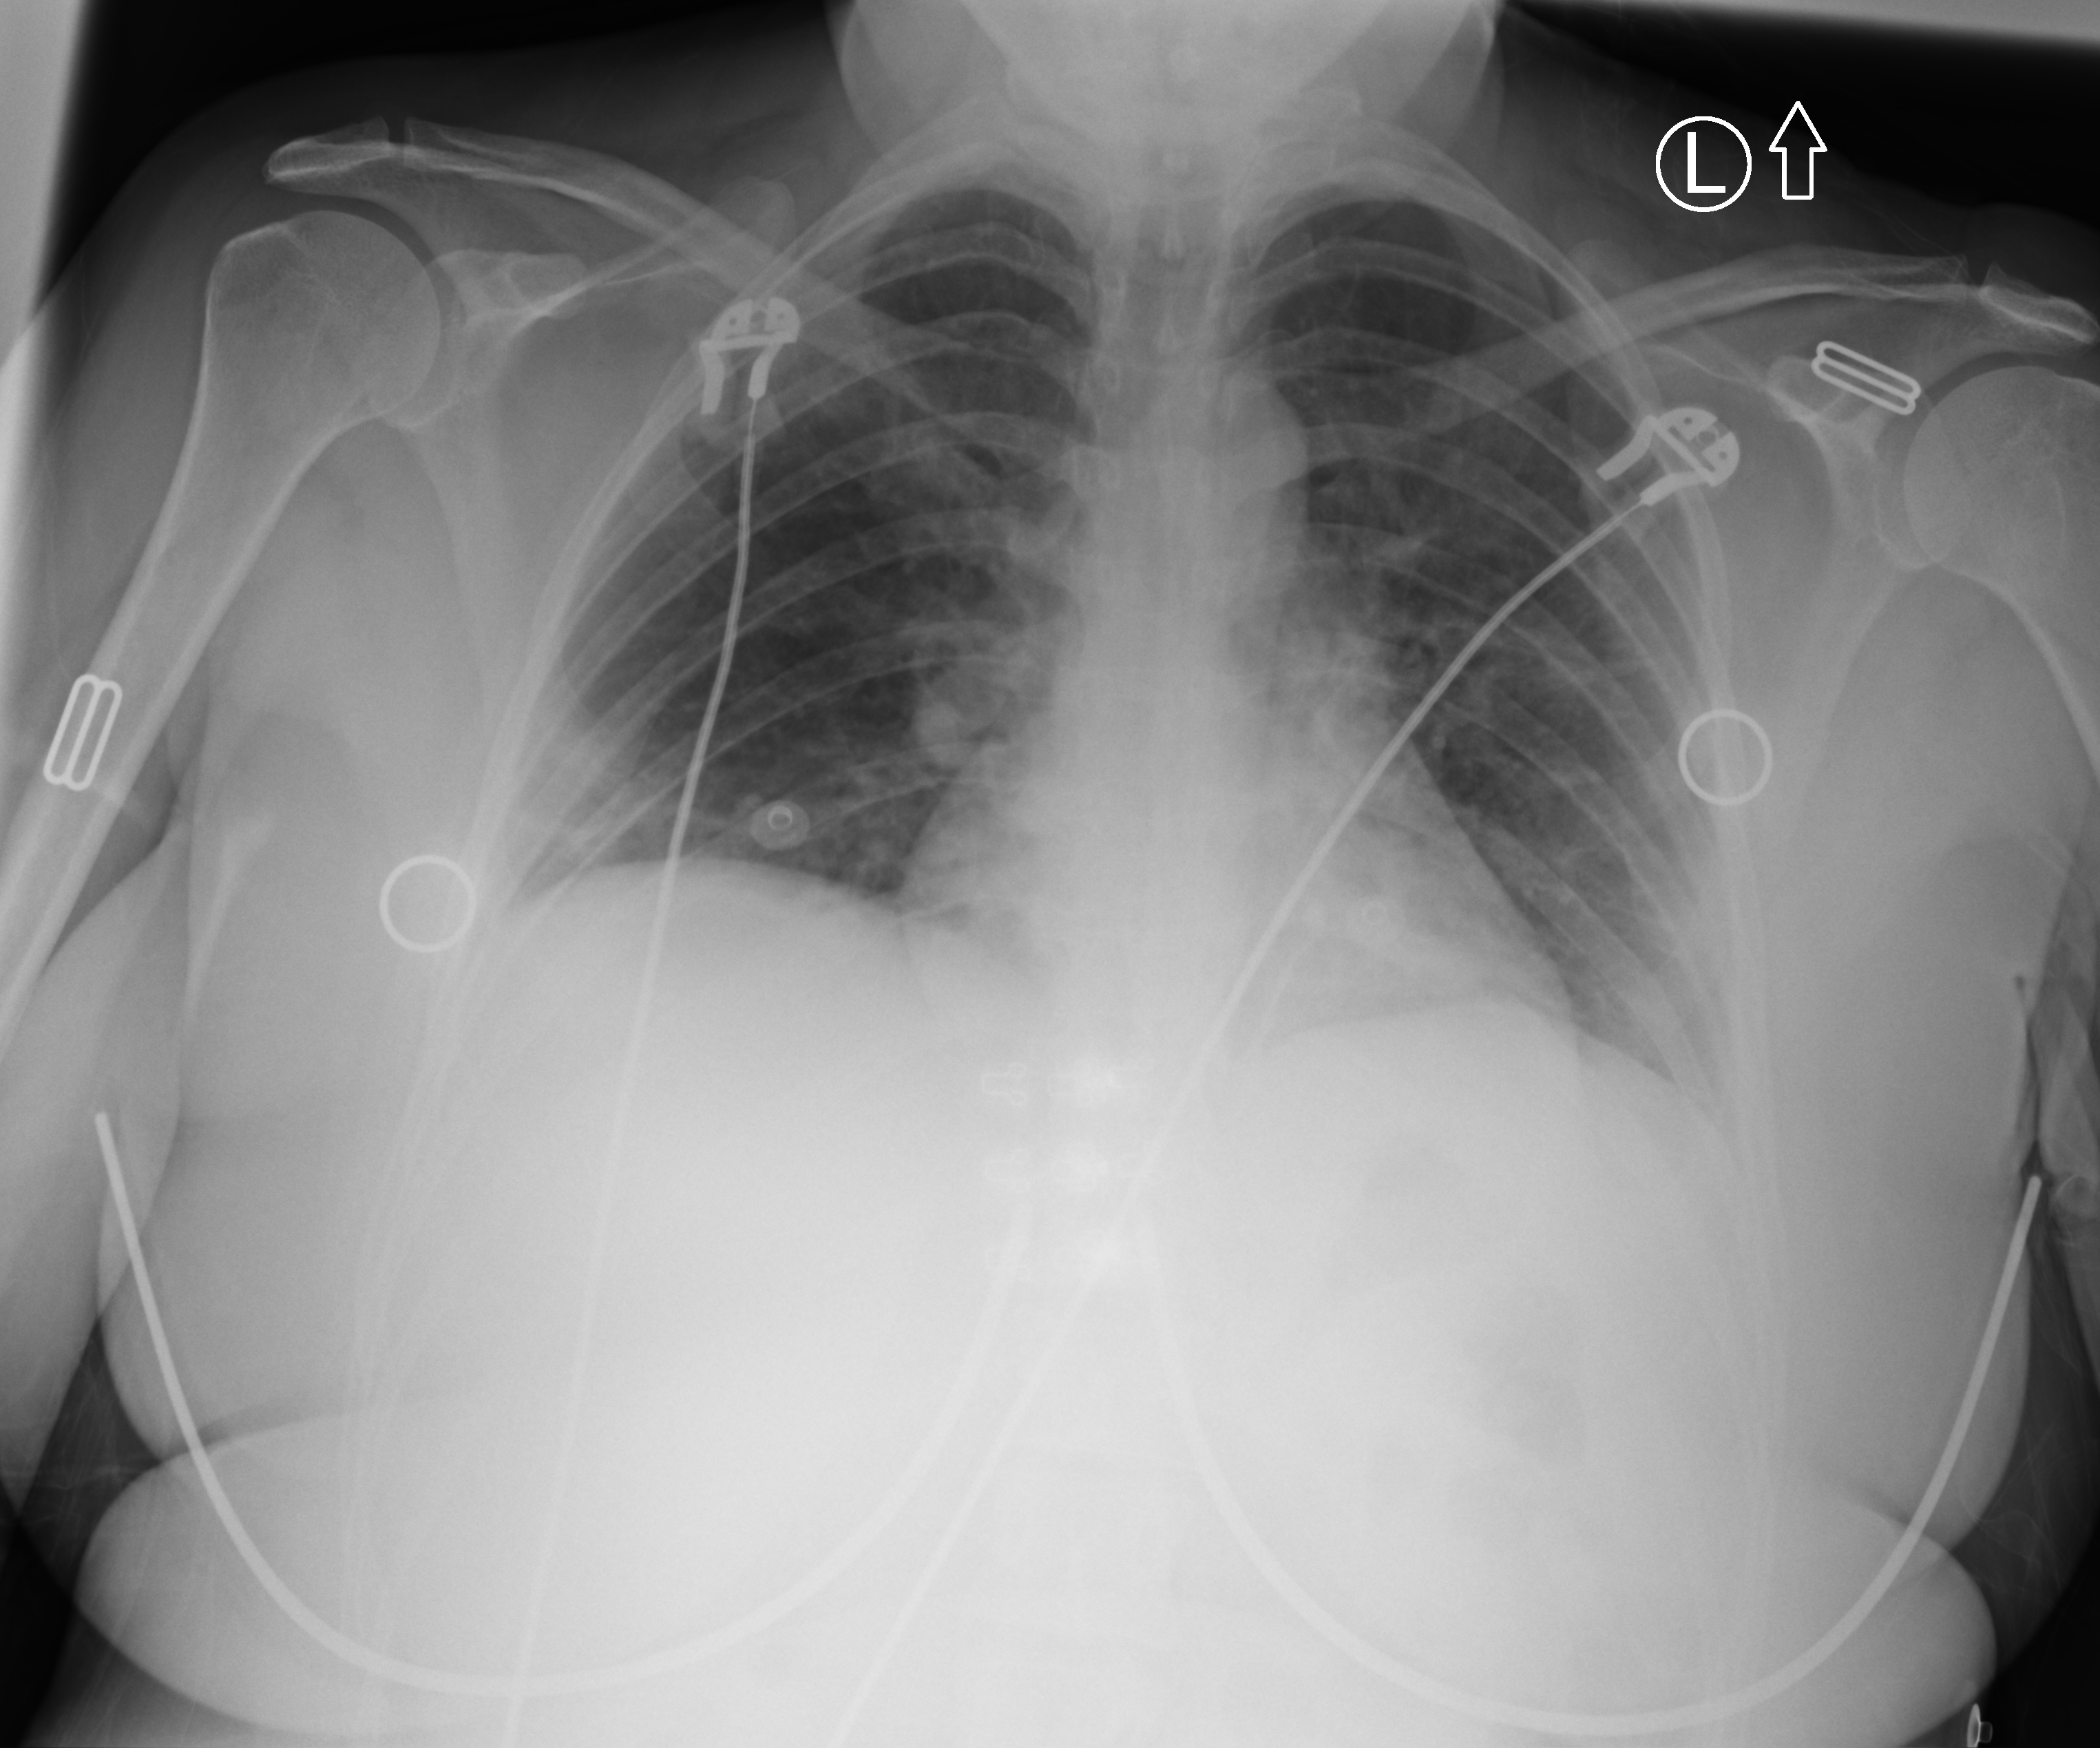
Portable chest radiograph, anteroposterior (AP) projection. Female patient hospitalised with COVID-19, age 18–59 years.
Hospital-stay facts (about this admission, not read from this image; timing relative to this image not recorded):
- mechanically ventilated during this hospital stay: no
- smoking status (admission record): never